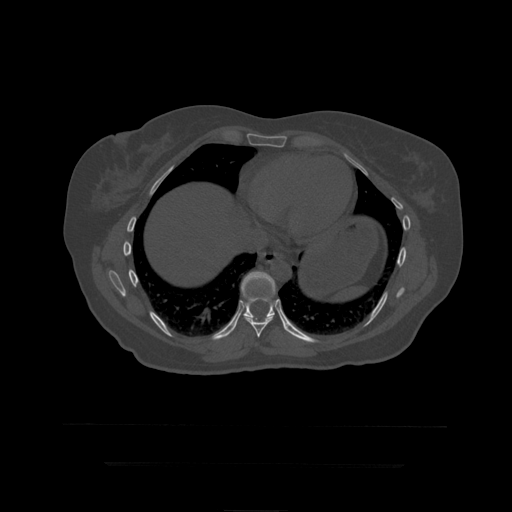
CT including the spine, one axial slice; position 253 of 399 along the scan axis; reconstruction kernel STANDARD; bone window (W 1800 / L 400 HU); 1.25 mm slice thickness; 512 × 512 image matrix. Patient age 41 years. From the clinical record (not read from this slice): primary cancer: breast.
Outlined on this slice (semi-automatic segmentation, software-assisted and operator-edited):
- T10 vertebra: bounding box [x1, y1, x2, y2] px = [241, 272, 288, 332]
- T9 vertebra: [243, 315, 274, 338]